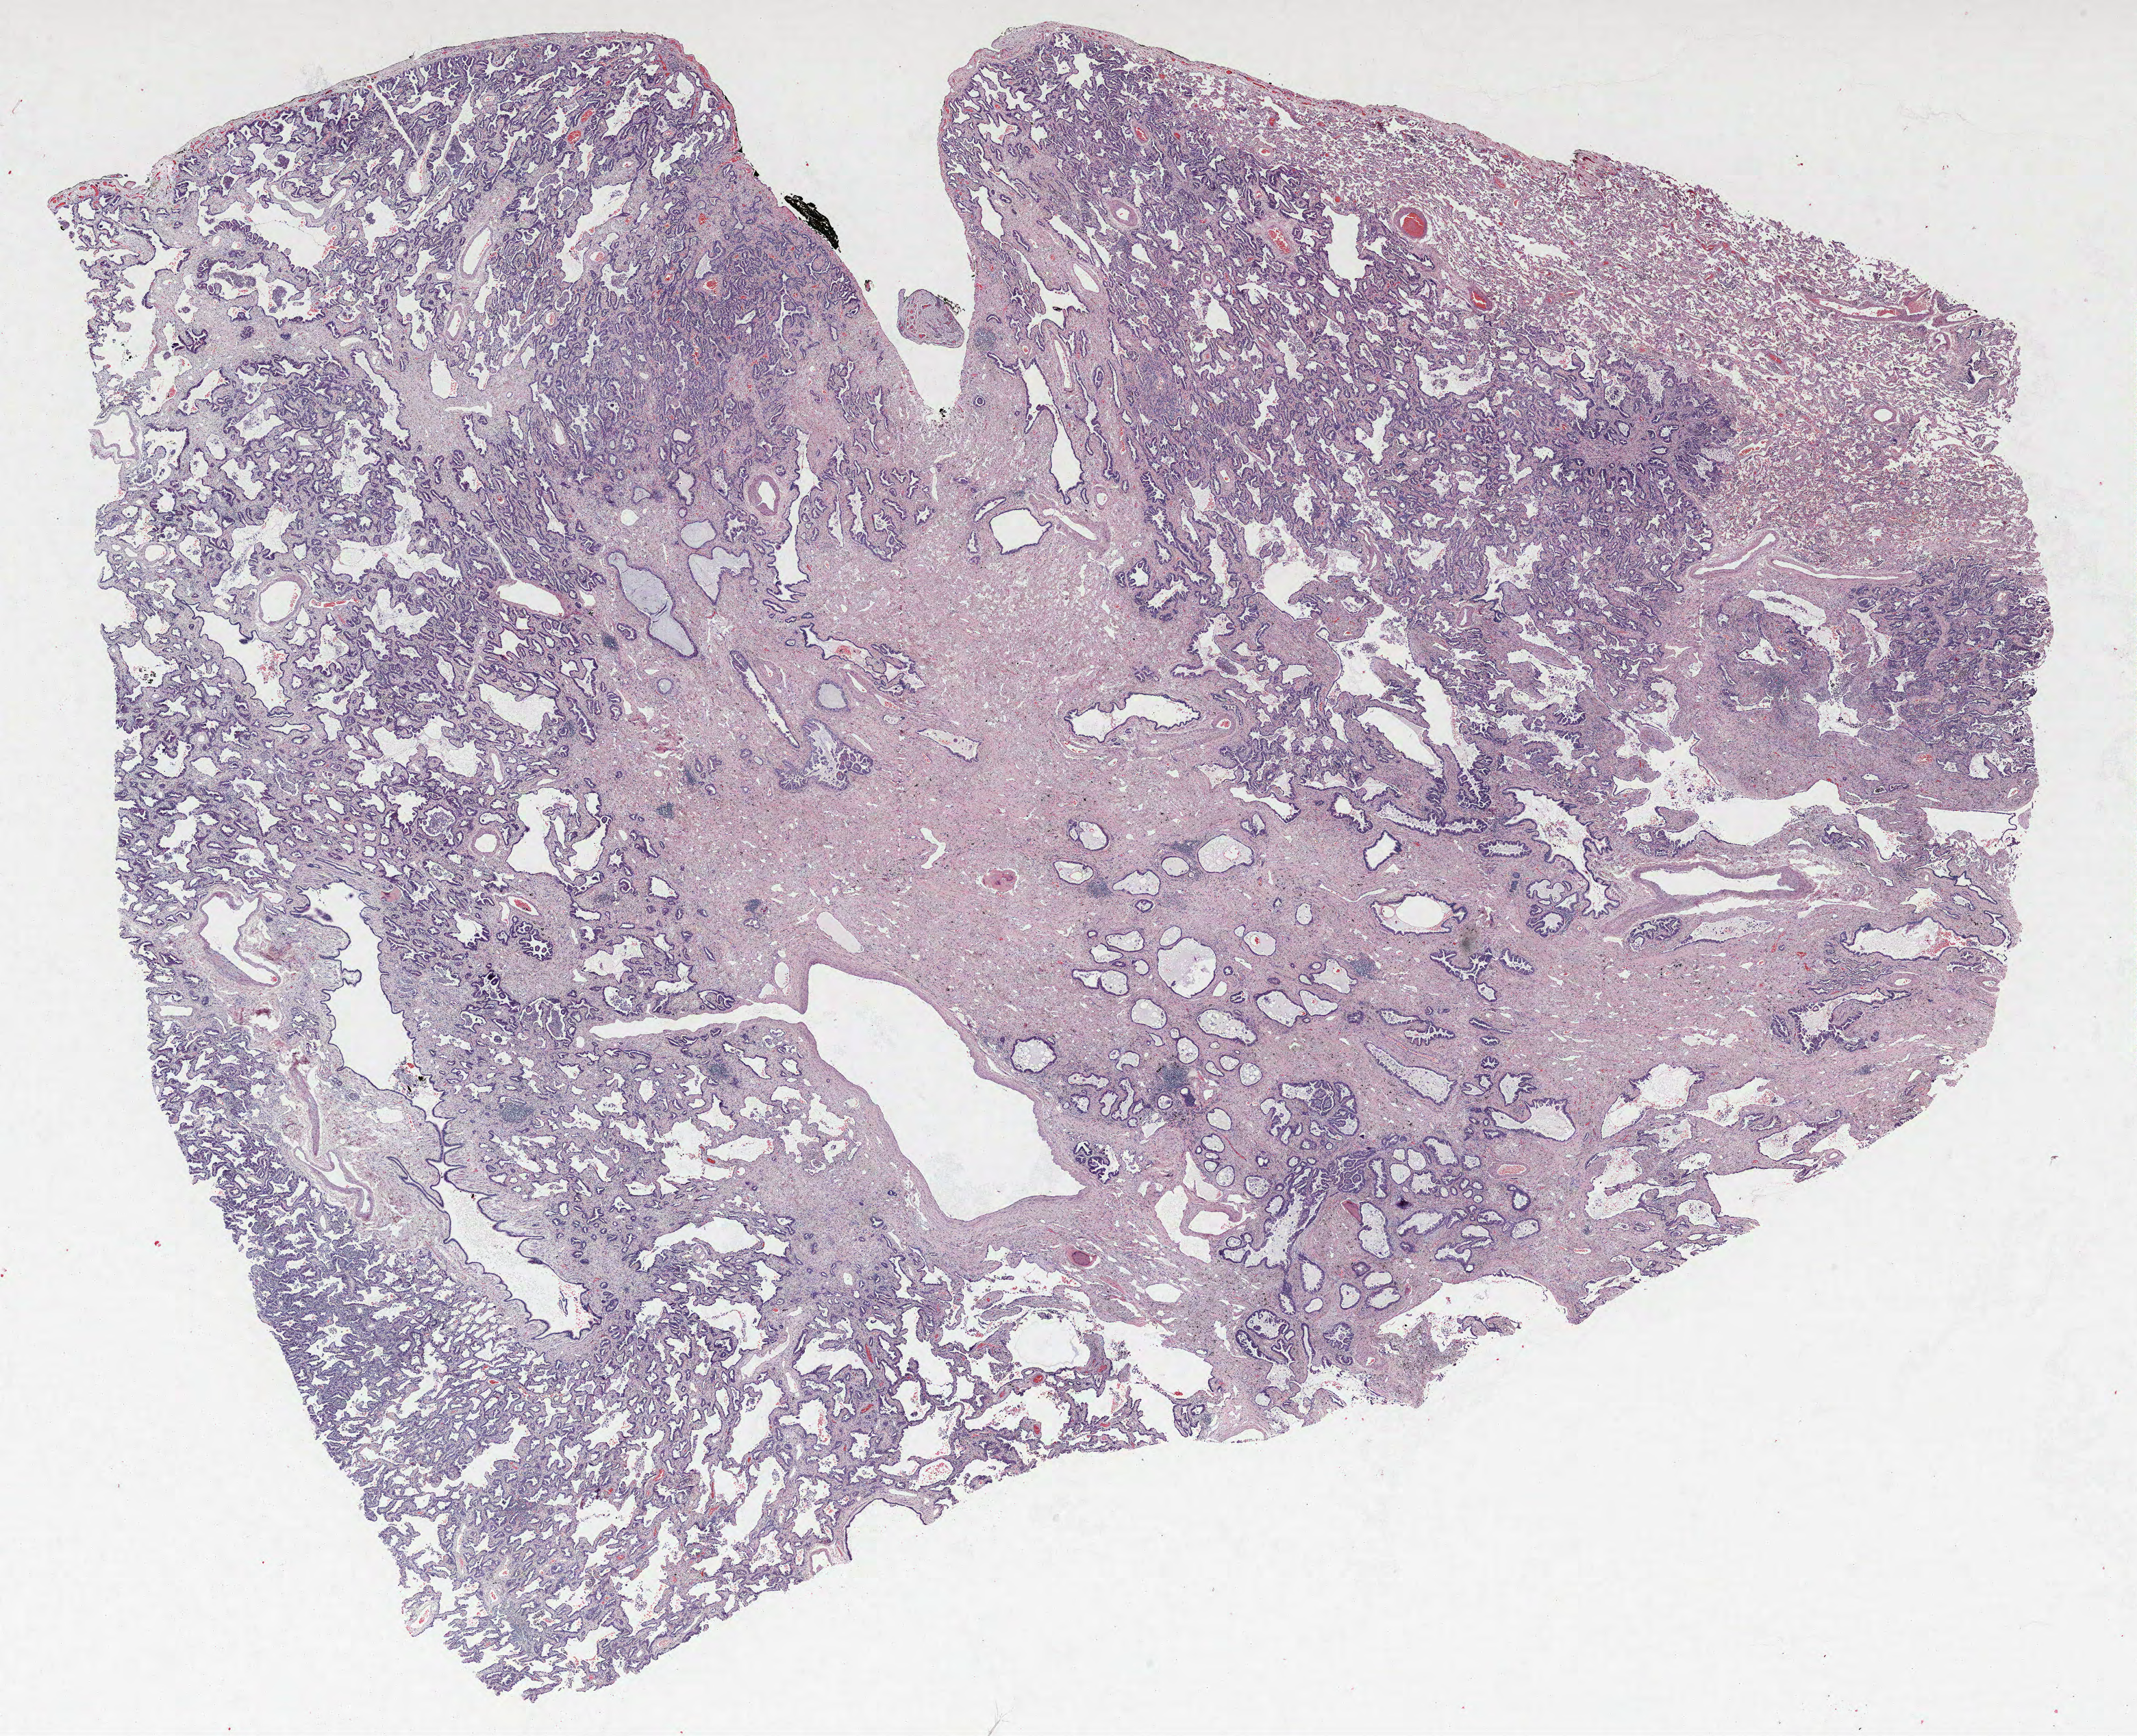
Hematoxylin and eosin (H&E) stained whole-slide image, whole scanned area (about 25.0 x 20.3 mm) shown as a low-resolution overview; formalin-fixed paraffin-embedded (FFPE) section; lung tissue. Male patient, aged 64 at enrolment. Grade: well differentiated (G1).
* tumour size (pathology): 45 mm
* participant's lung-cancer diagnosis: Adenocarcinoma, NOS
* stage (AJCC 6th edition): IB
* primary tumour location (clinical record): right upper lobe